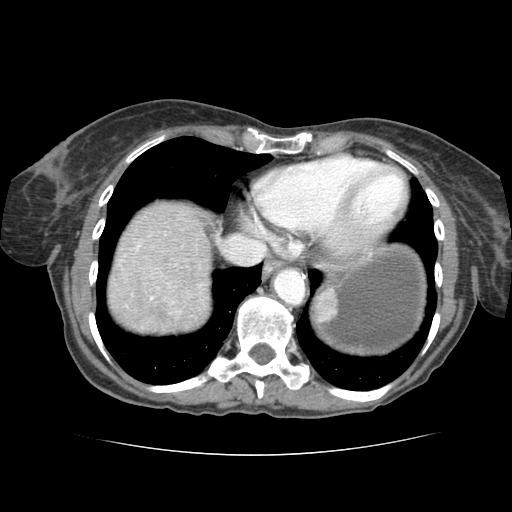
Contrast-enhanced abdominal CT (liver protocol), one axial slice. Position 72 of 77 along the scan axis. Reconstruction kernel STANDARD. Soft-tissue window (W 400 / L 40 HU). 512 × 512 image matrix, field of view 340 × 340 mm. From the clinical record (not read from this slice): diagnosis: hepatocellular carcinoma (patient treated with transarterial chemoembolisation; whether this scan precedes or follows treatment is not stated here); TNM stage (as recorded): Stage-I; Child-Pugh class: A; tumour differentiation: well differentiated; tumour nodularity: uninodular.
Outlined on this slice (semi-automatically segmented with operator editing):
- abdominal aorta: bounding box (x1, y1, x2, y2) in pixels: (274, 268, 305, 304)
- liver parenchyma outside the tumour (the mass and vessels are separate outlines, so this box may not span the whole liver): (114, 210, 206, 316)